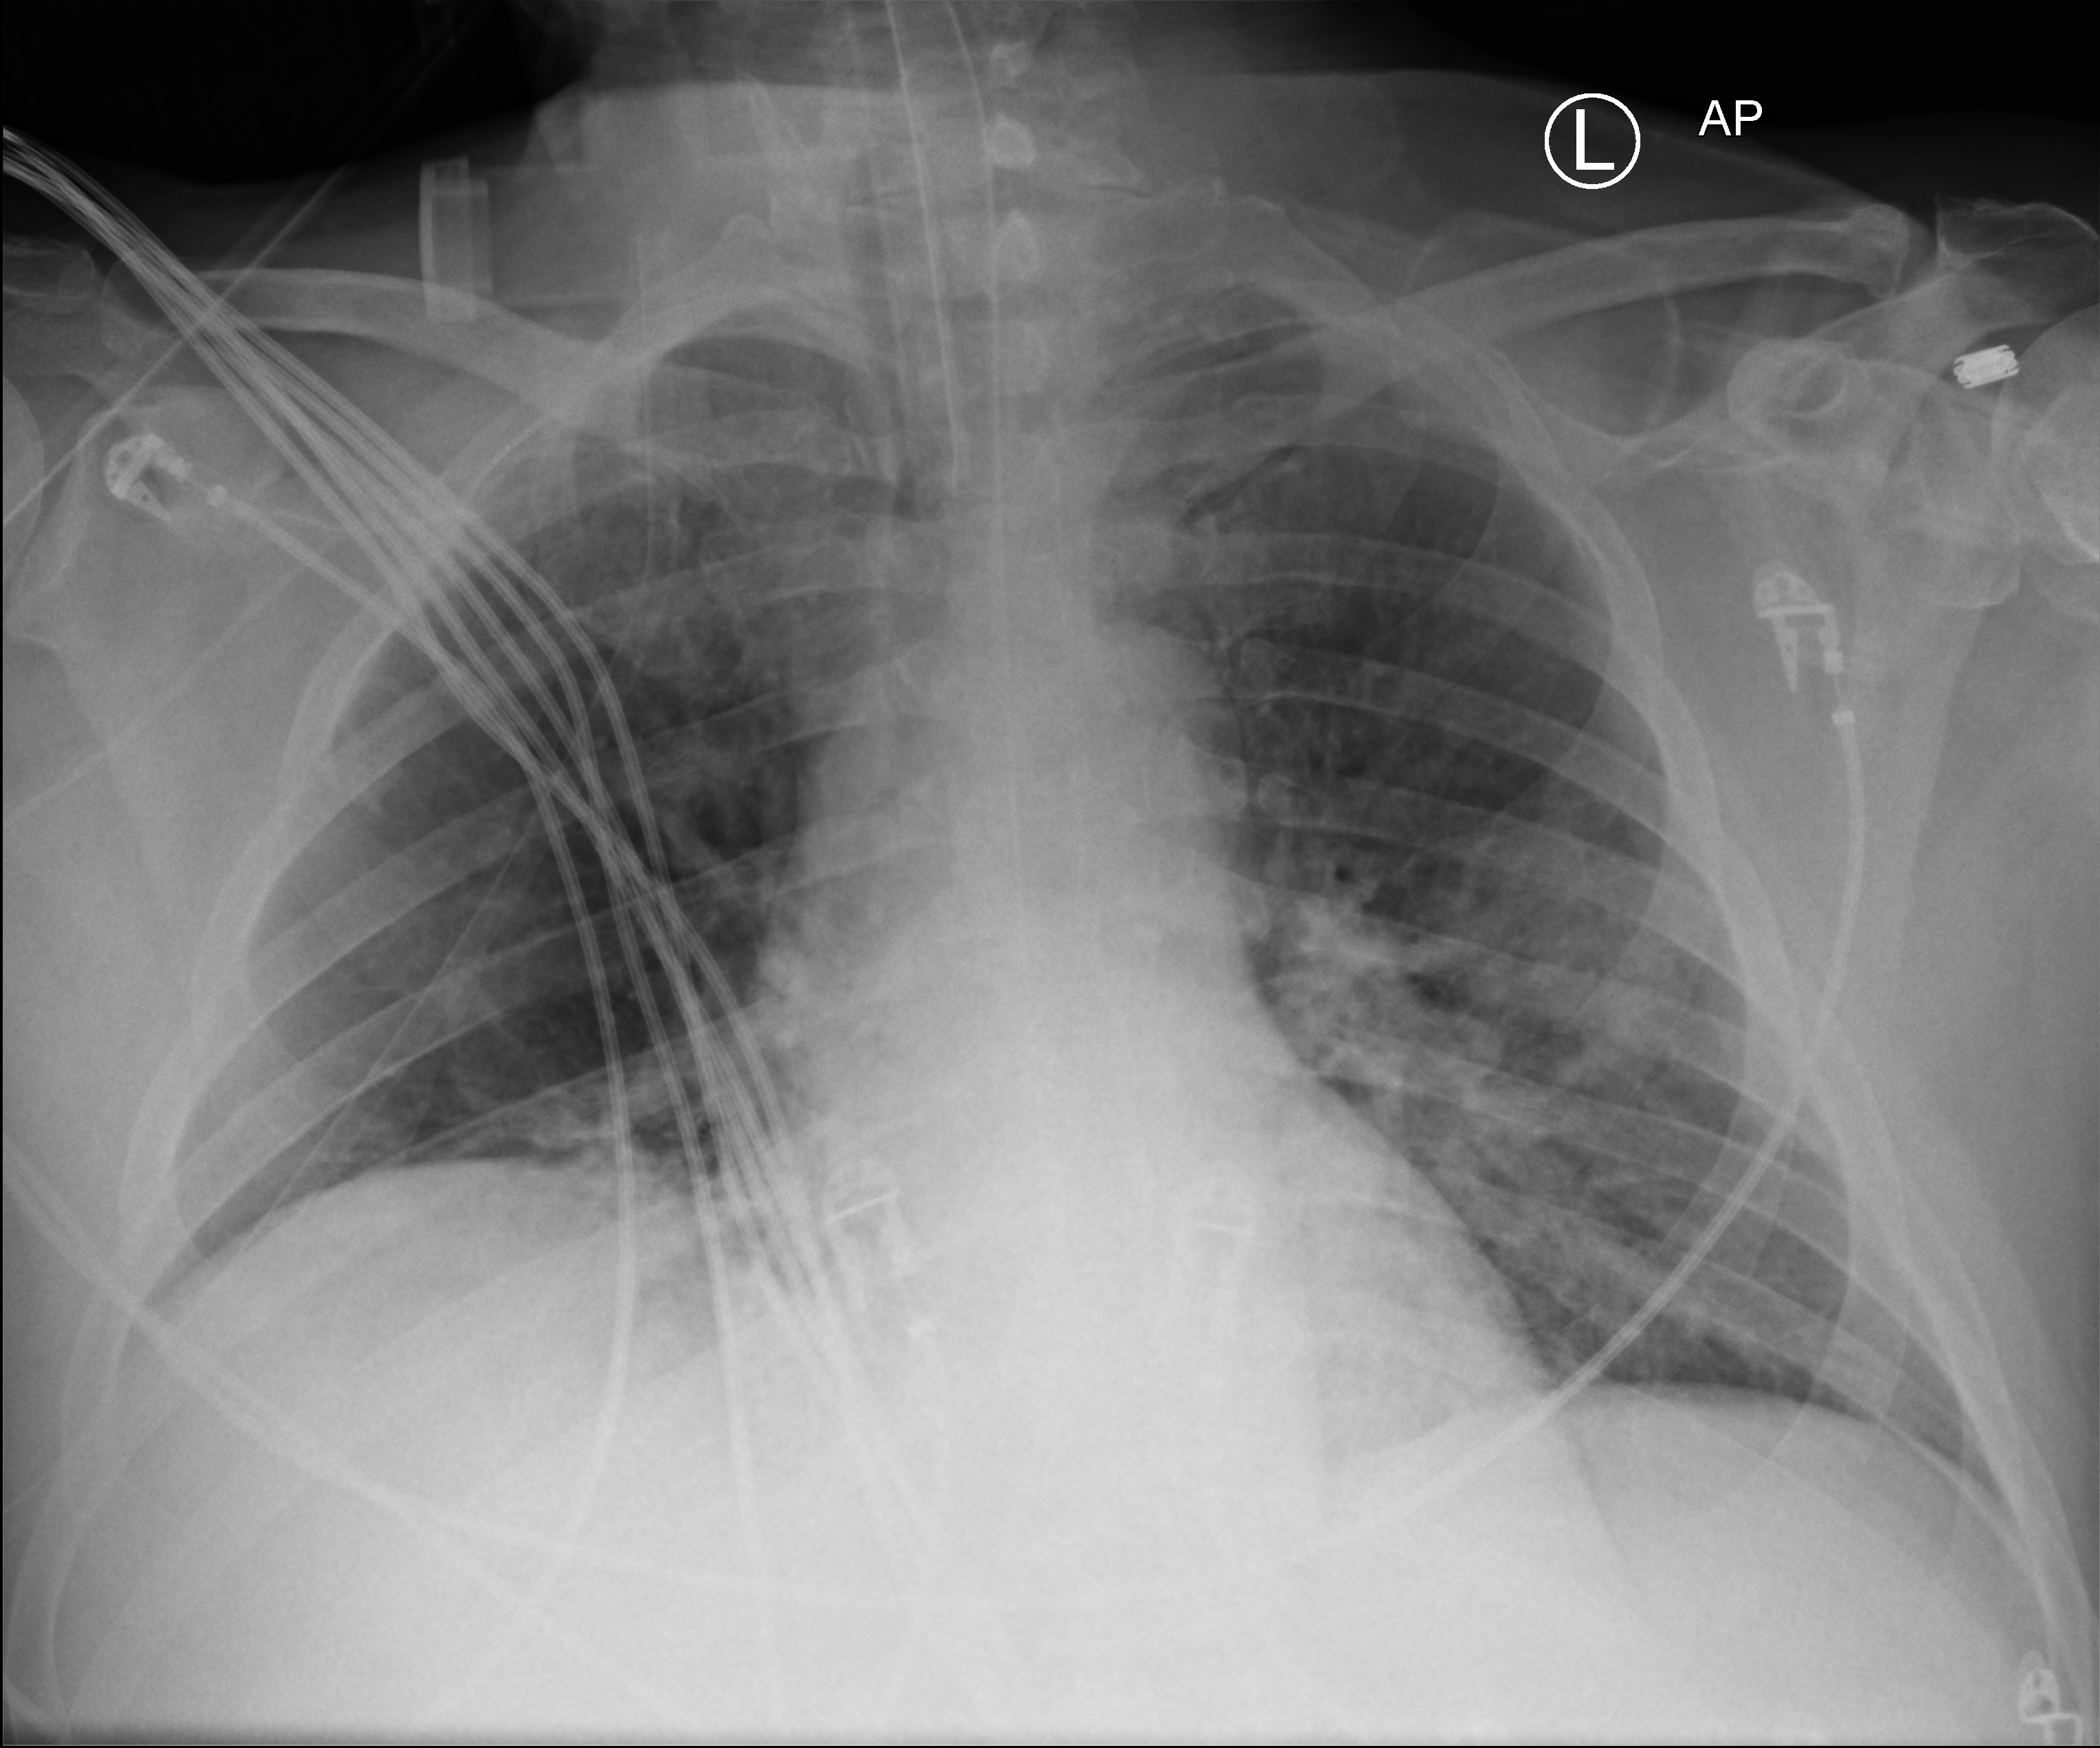
Chest X-ray (portable); anteroposterior (AP) projection. Male patient hospitalised with COVID-19, age 18–59 years.
Hospital-stay facts (about this admission, not read from this image; timing relative to this image not recorded):
- admitted to intensive care during this hospital stay: yes
- length of hospital stay: 28 days